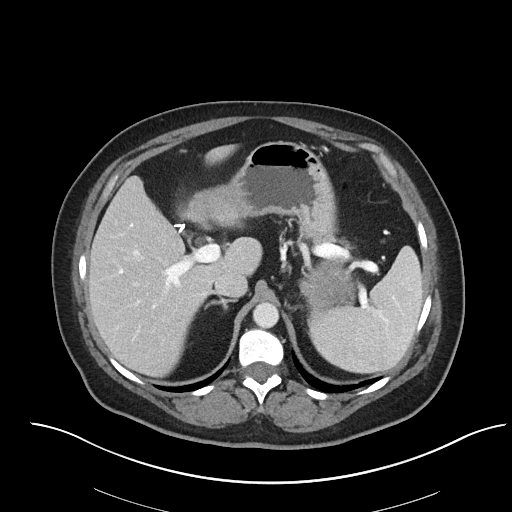
Contrast-enhanced abdominal CT, one axial slice. Reconstruction kernel I40f/2. Intravenous contrast given. Soft-tissue window (W 400 / L 40 HU). 512 × 512 image matrix. Female patient, age 53 years. From the clinical record (not read from this slice): diagnosis: adrenocortical carcinoma; tumour side: left adrenal; tumour size at pathology: 9 cm; Ki-67 index: 28 %; stage (as recorded): 2.
Structures marked on this image (semi-automatic segmentation, software-assisted and operator-edited):
- mass: bounding box [x1, y1, x2, y2] px = [300, 262, 355, 314]